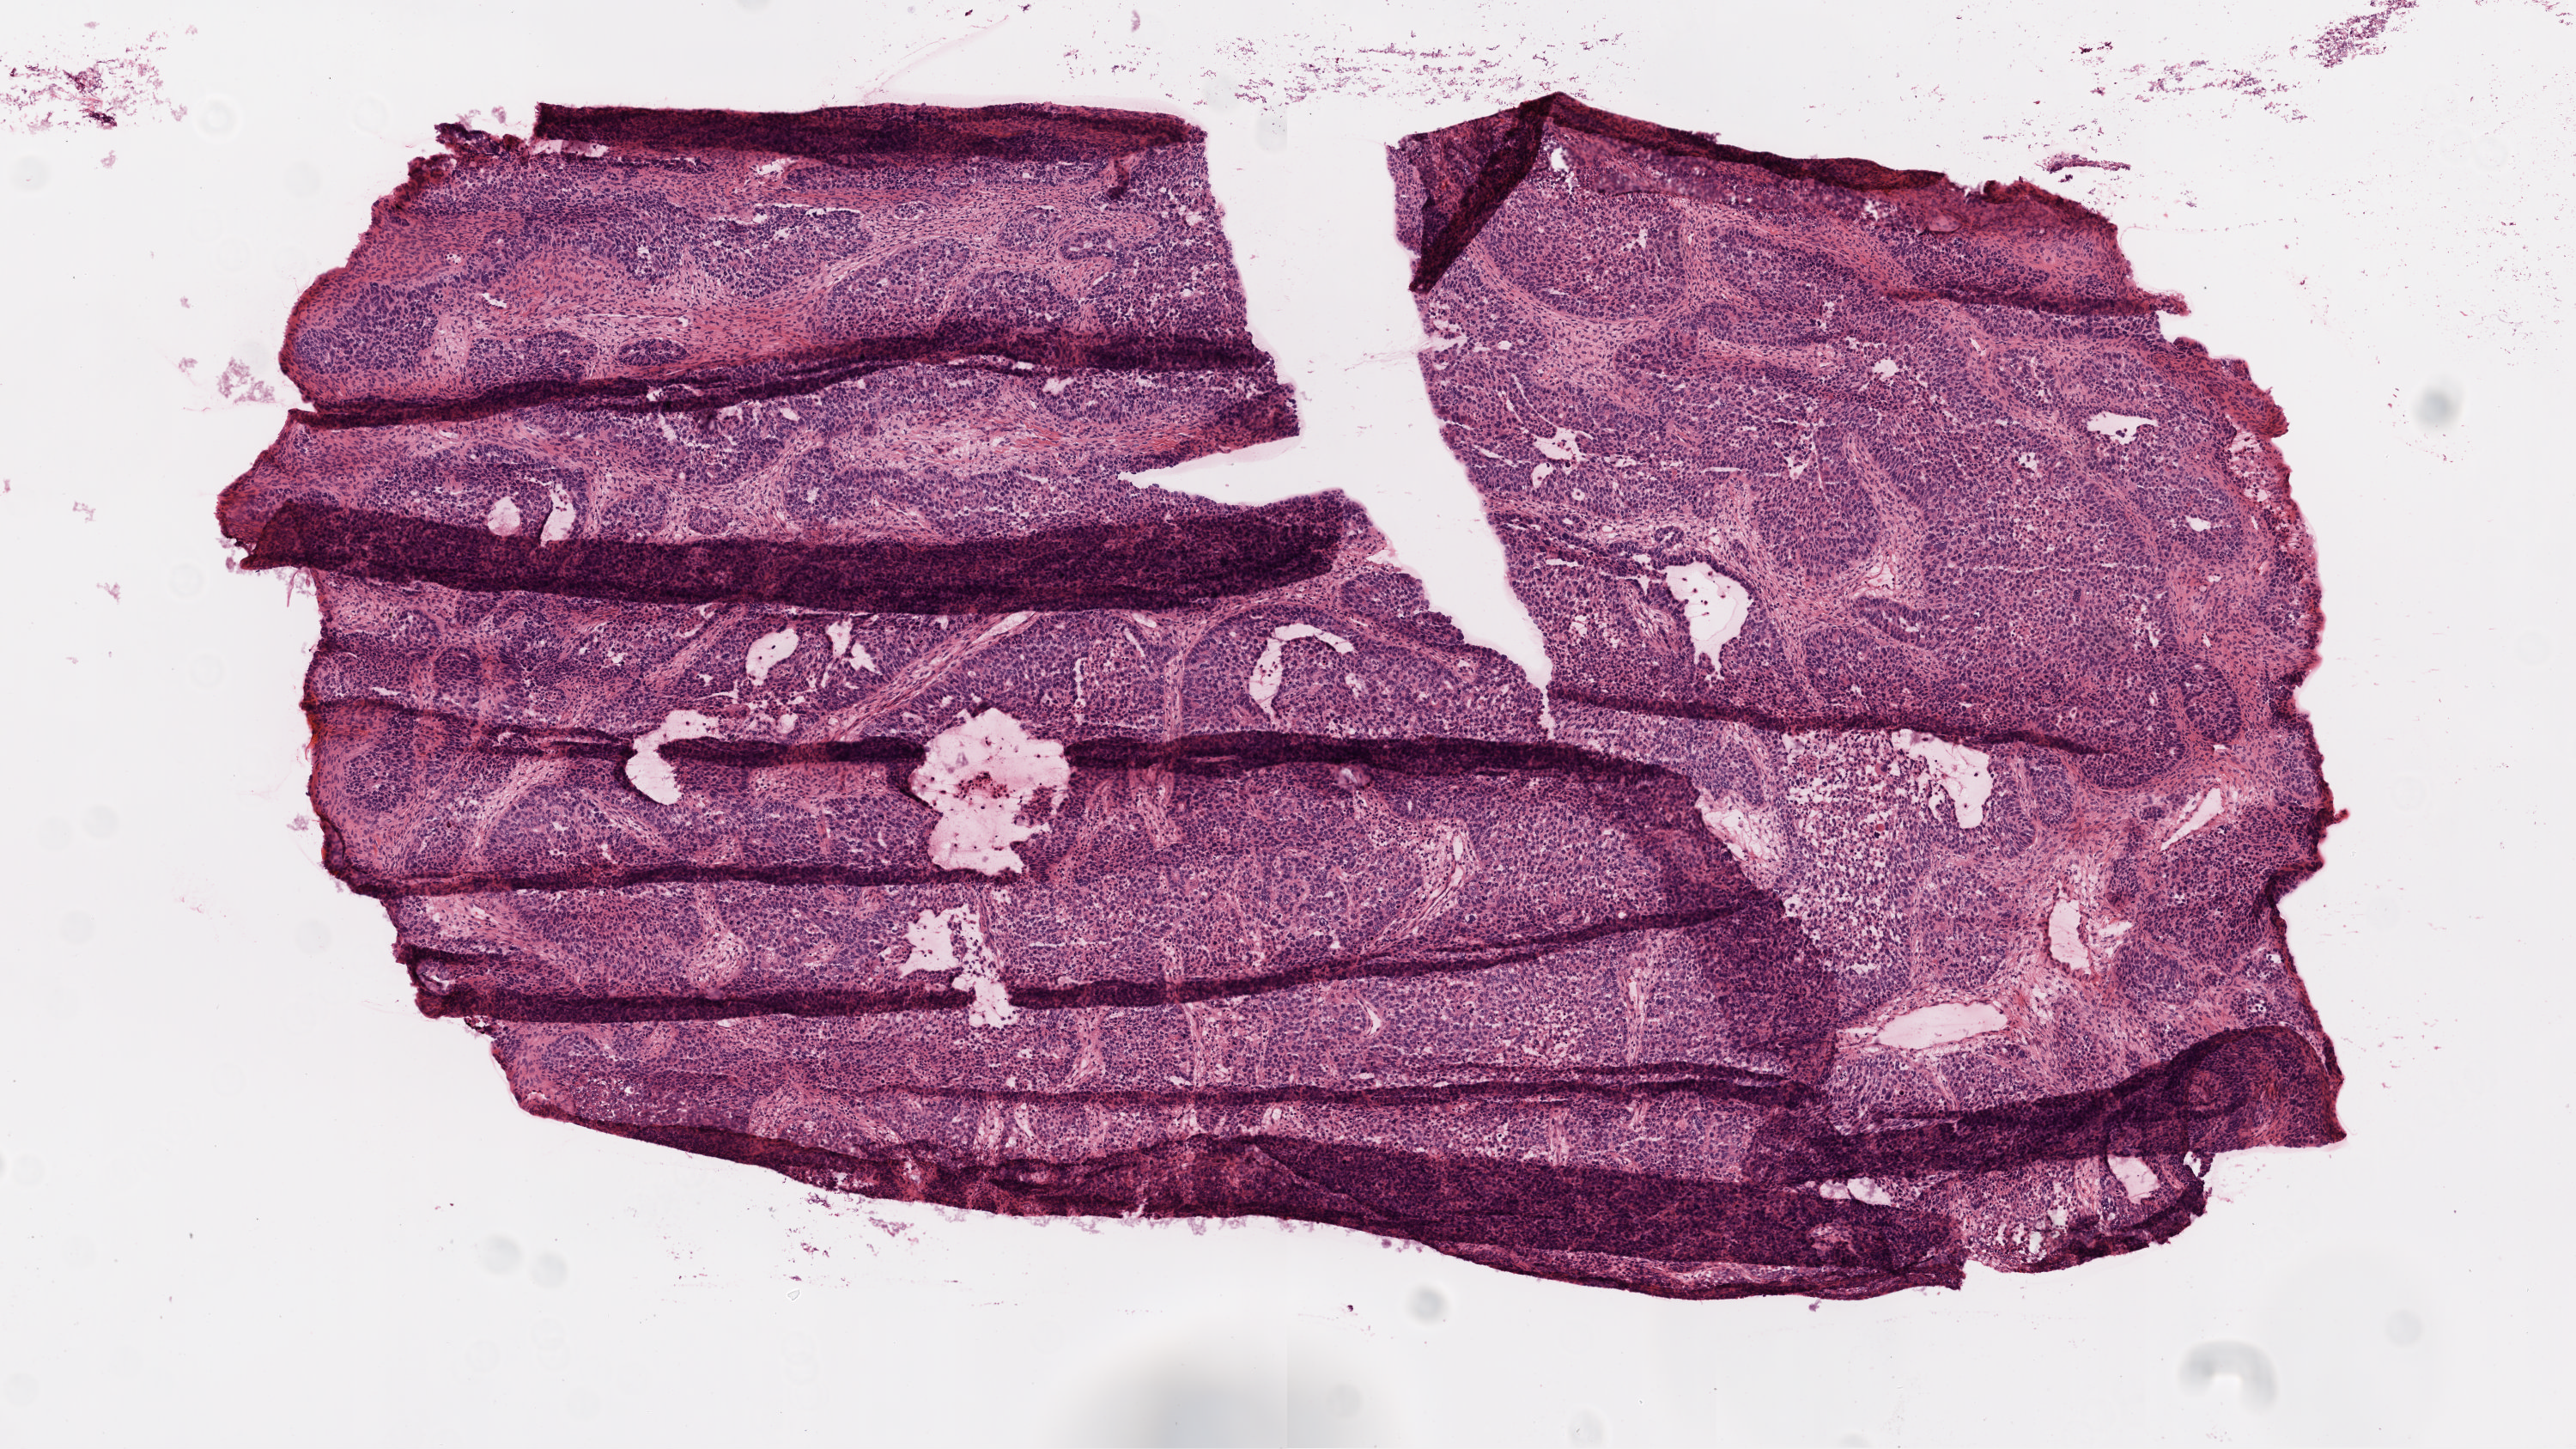
Digitized Hematoxylin and eosin (H&E) stained tissue section (whole slide), a low-resolution overview of the entire scanned area, about 6.0 x 3.4 mm; frozen section from the top of the tissue portion; sample: primary tumour, ovary. Patient: female, age at initial diagnosis 45 years. Histologic grade: G3 (poorly differentiated). Pathologist review of this section (percent, as recorded): tumour cells 80%, tumour nuclei 95%, normal cells 0%, stromal cells 19%, necrosis 1%. Inflammatory infiltration, as recorded: lymphocyte infiltration 1%.
FIGO stage: IIIC. Histologic diagnosis: Serous cystadenocarcinoma, NOS.